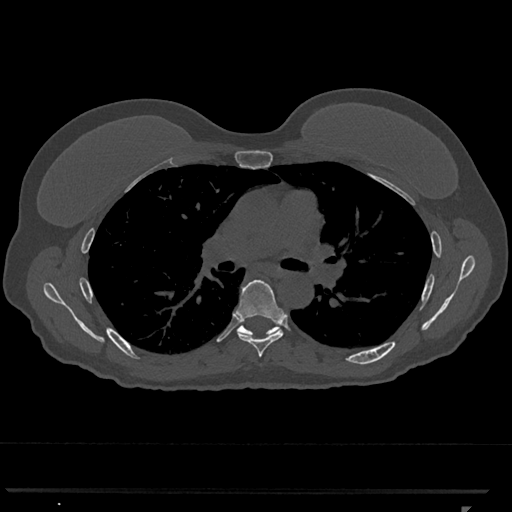
CT including the spine, one axial slice. Position 749 of 793 along the scan axis. Bone window (W 1800 / L 400 HU). 0.5 mm slice thickness. 512 × 512 image matrix, field of view 380 × 380 mm. Patient: female, 62 years. From the clinical record (not read from this slice): primary cancer: renal.
Structures marked on this image (semi-automatic segmentation, software-assisted and operator-edited):
- T6 vertebra: box from (x=236, y=279) to (x=285, y=357) px
- T7 vertebra: (x=237, y=323)–(x=279, y=336)